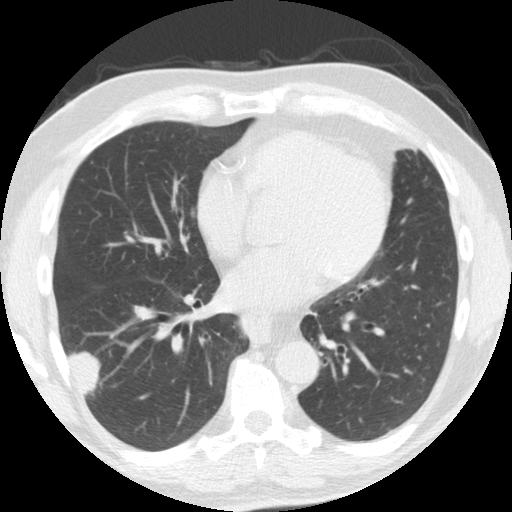
Chest CT (low-dose screening protocol), one axial image. Second screening round (one year after baseline). Lung window (W 1500 / L -600 HU). 512 × 512 image matrix. Male participant, aged 61 years at enrolment. Former smoker at enrolment.
Expert-annotated lung lesion, bounding box [x1, y1, x2, y2] px = [47, 323, 115, 399]. Reader record for this screening exam (exam-level; its link to the box is not recorded): non-calcified nodule or mass ≥4 mm, right lower lobe, 33 × 19 mm, smooth margins, soft tissue attenuation, pre-existing on the prior screen: yes; interval growth: yes. Official screen result: positive, change unspecified: nodule(s) >= 4 mm or enlarging nodule(s), mass(es), or other non-specific abnormalities suspicious for lung cancer. Later outcome: lung cancer diagnosed 30 days after this screen — adenosquamous carcinoma, right lower lobe, poorly differentiated (G3), stage IV (AJCC 6th edition), 45 mm at pathology.